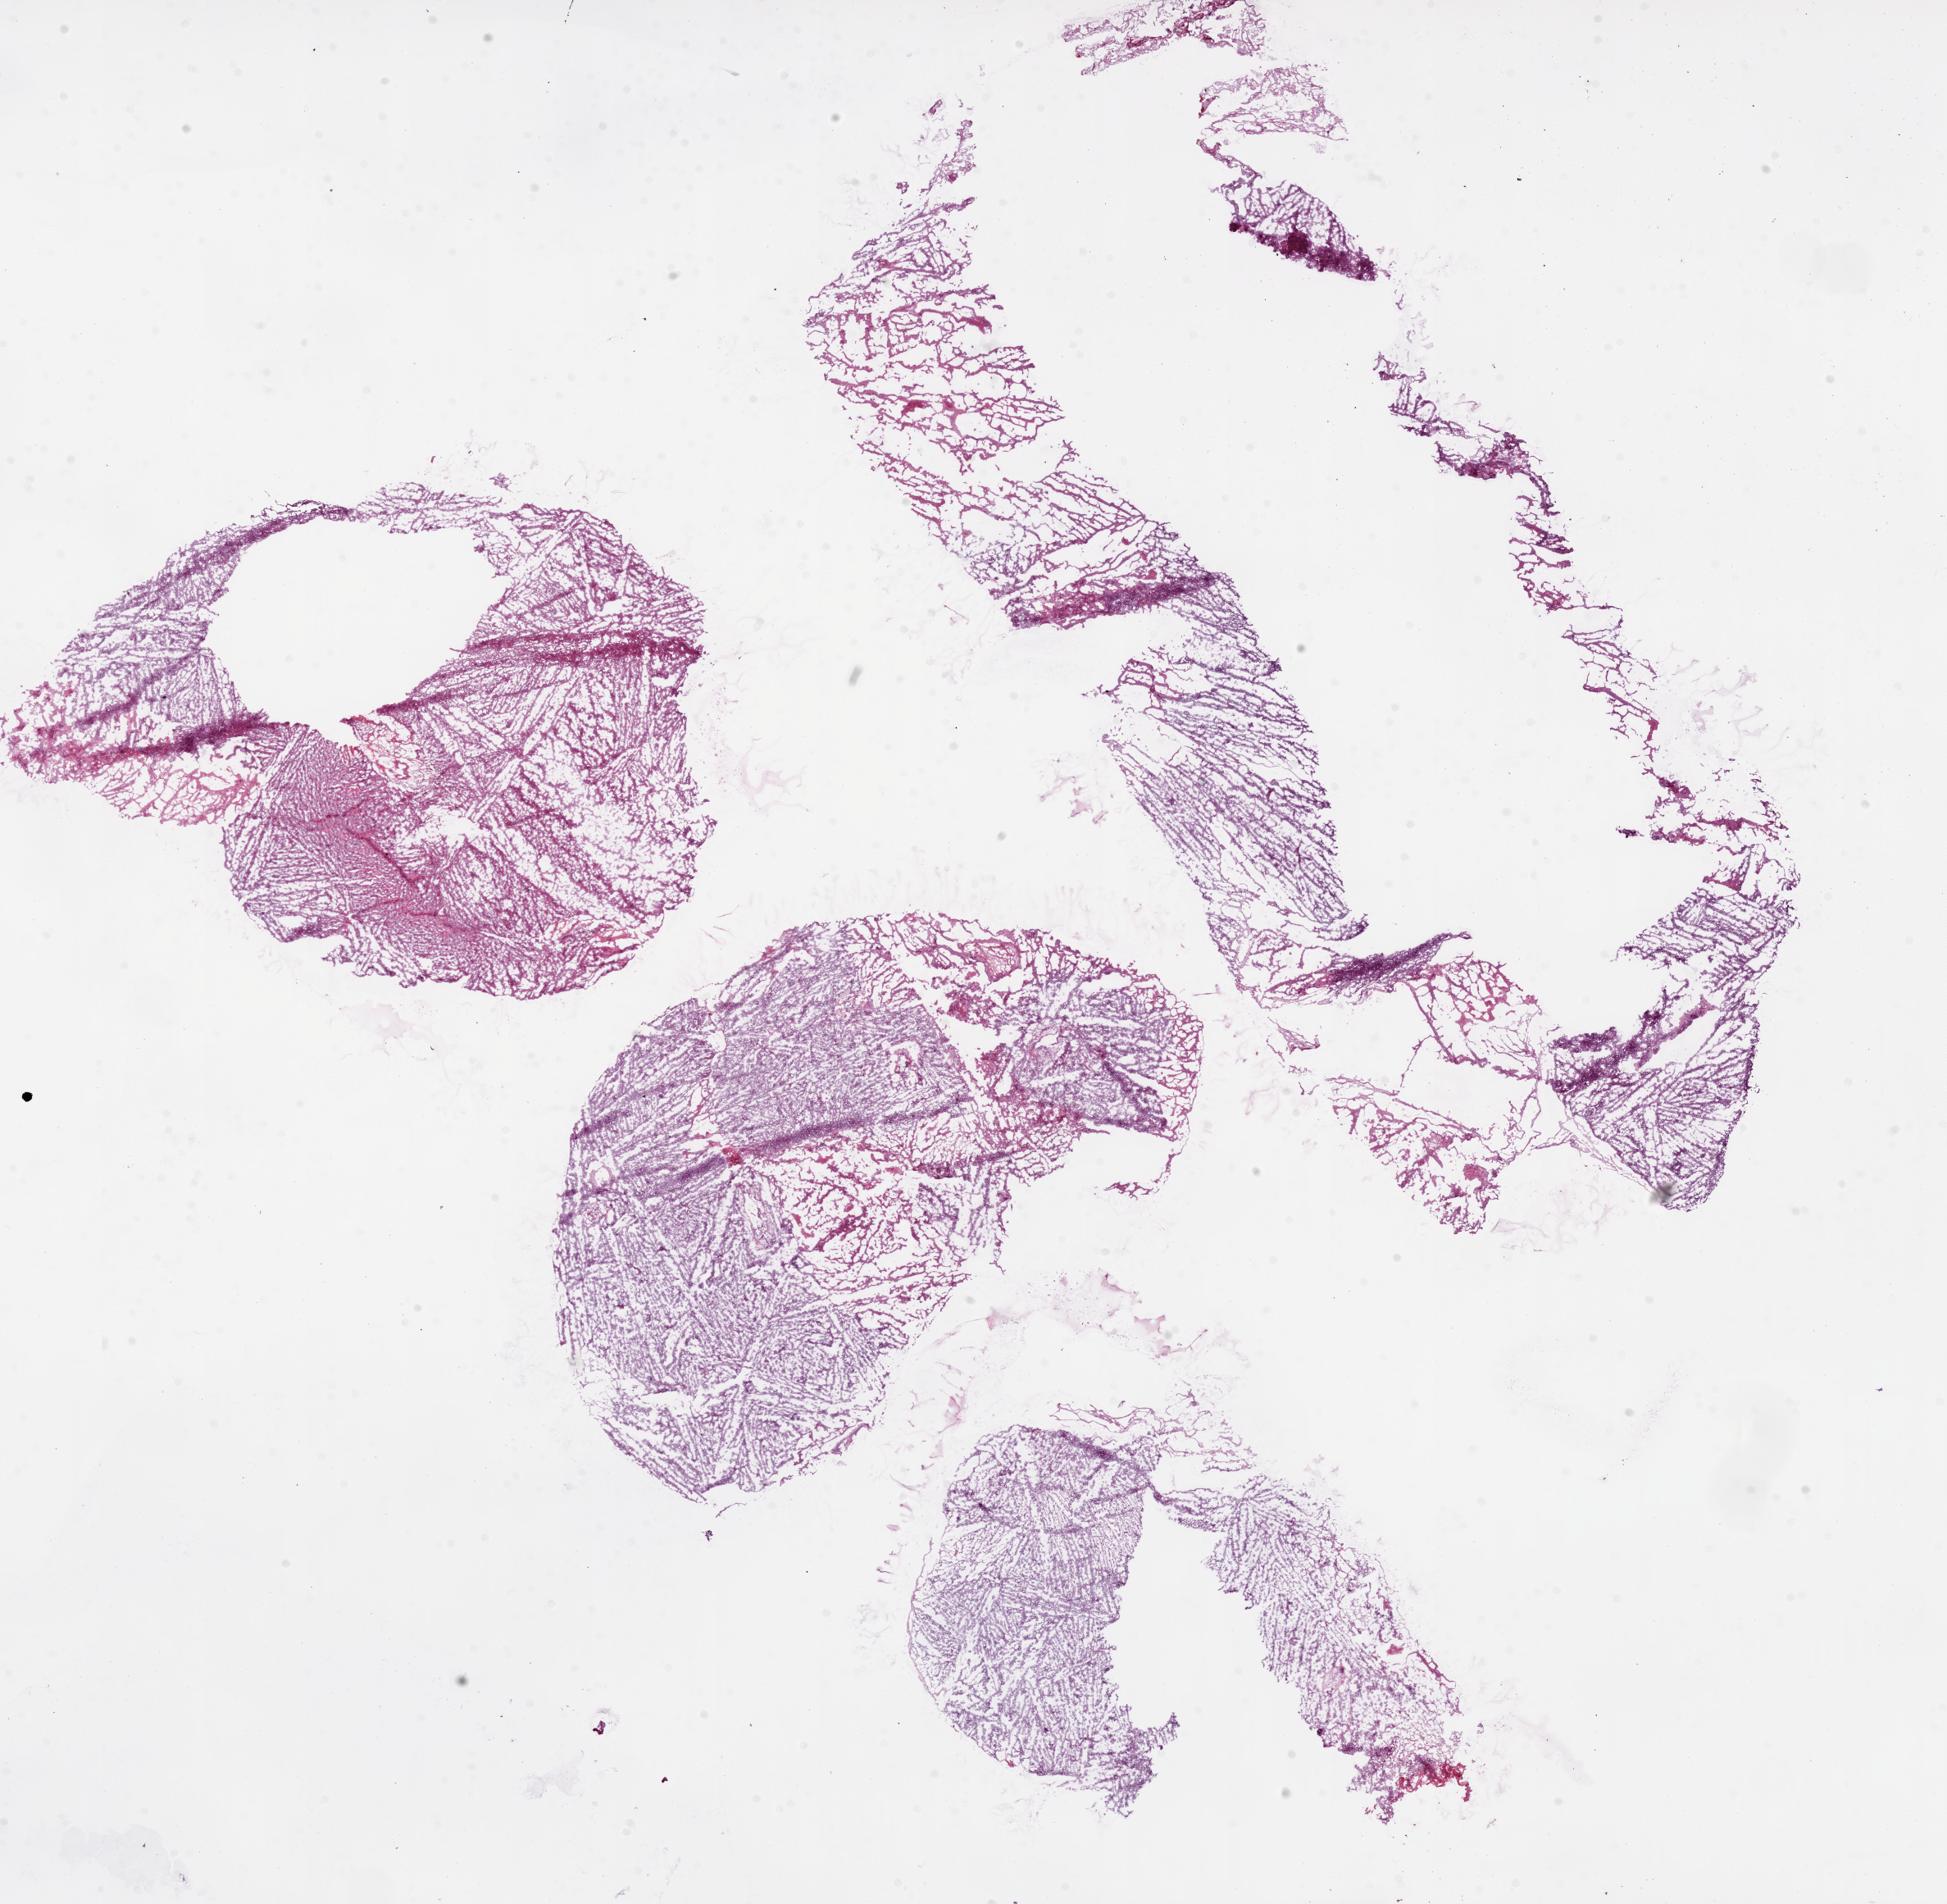
Digitized H&E-stained tissue section (whole slide), whole scanned area (about 19.1 x 18.6 mm, from a 20x scan) shown as a low-resolution overview; frozen section; brain, primary tumour sample. Patient: male, age at initial diagnosis 58 years. Slide review estimates, as recorded: tumour cells 80%, tumour nuclei 70%, normal cells 0%, stromal cells 0%, necrosis 20%.
Diagnosis: Glioblastoma.